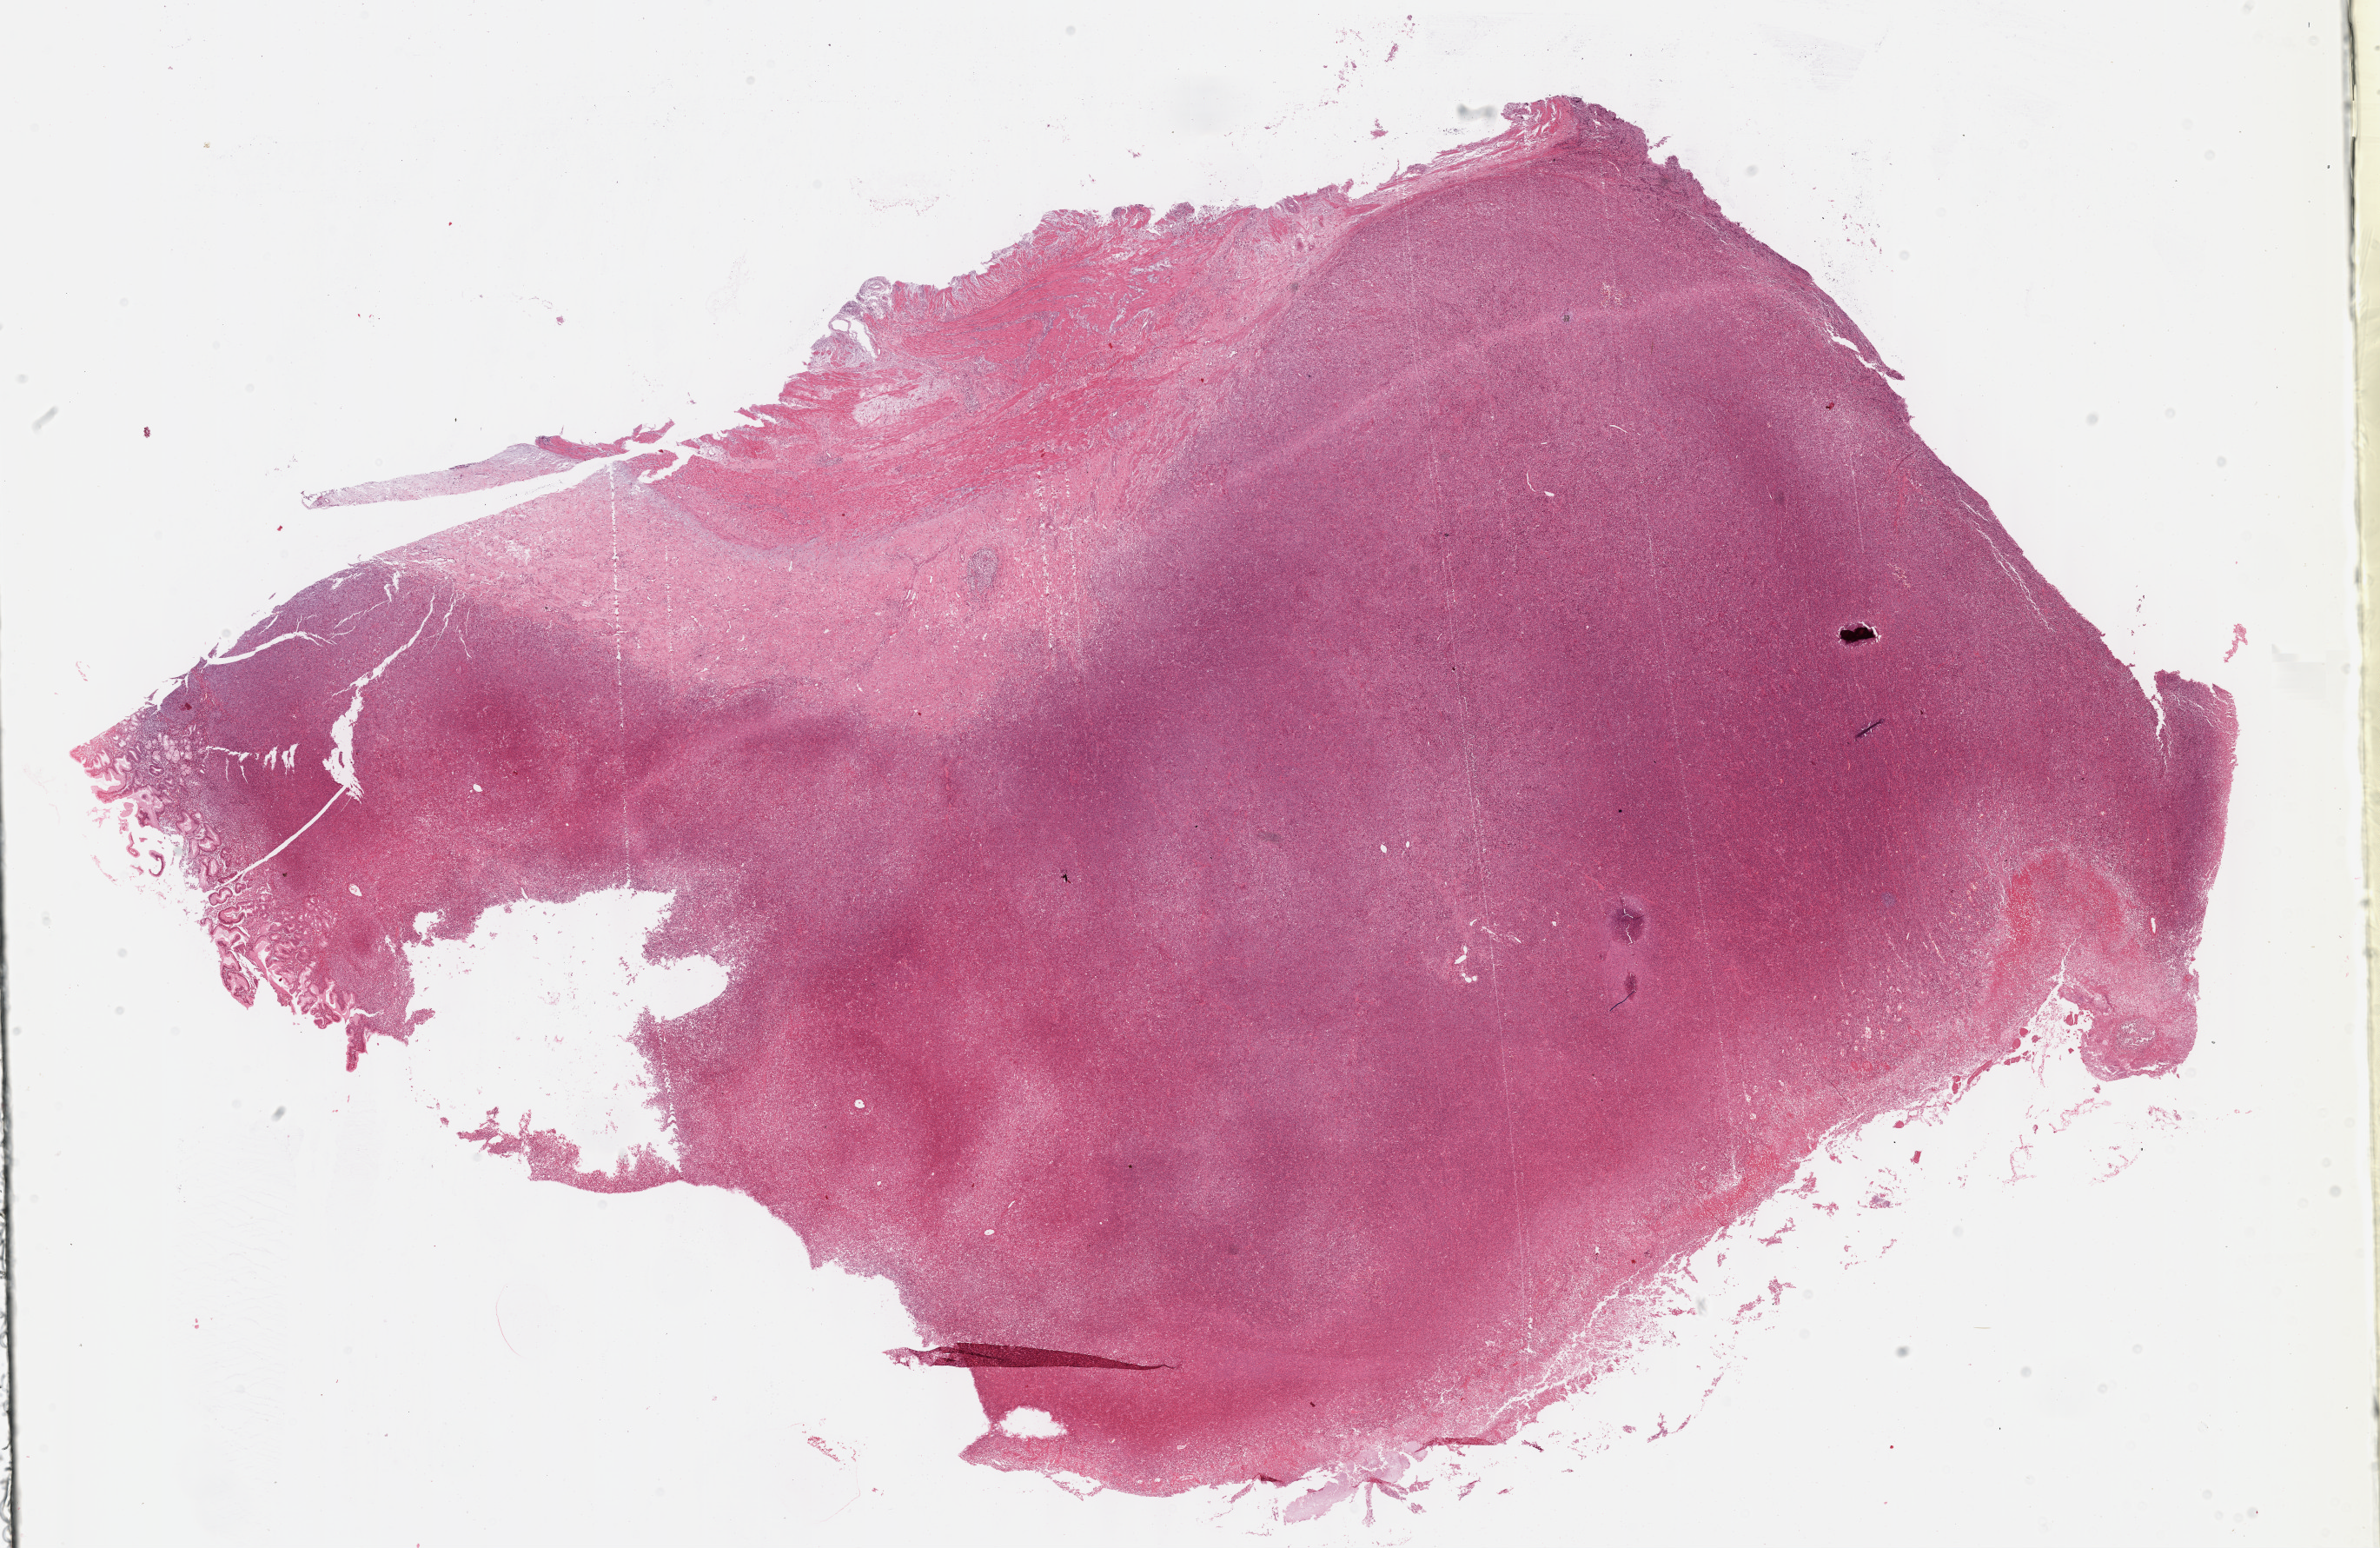
Digitized H&E tissue section (whole slide), low-resolution overview of the scanned area, about 22.1 x 14.4 mm. Formalin-fixed paraffin-embedded (FFPE) diagnostic section. Stomach, primary tumour sample. Female, age 66 years at initial diagnosis. Histologic grade: G3 (poorly differentiated).
Lymph nodes positive (case pathology): 2 of 7 examined. AJCC pathologic stage: IIIA (6th edition). Pathologic diagnosis: Carcinoma, diffuse type (fundus of stomach).